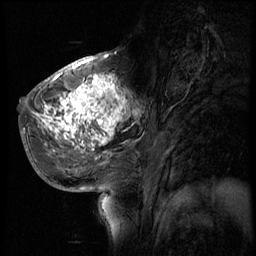
Breast MRI (dynamic contrast-enhanced), one sagittal slice. Slice 25 of 56 in the series (ordered by position). 4 images stored at this slice position (order not interpretable as contrast timing). 1.5 T. TE 4.2 ms, TR 8.9 ms. 2.5 mm slice thickness. 256 × 256 image matrix, field of view 220 × 220 mm. Patient: female, 51 years. From the clinical record (not read from this slice): setting: breast cancer imaged before/during neoadjuvant chemotherapy; receptor status: triple-negative.
Outlined on this slice (semi-automatic segmentation, software-assisted and operator-edited):
- analysis volume of interest (the breast-tissue region the enhancement analysis was run in; not a lesion): box from (x=30, y=70) to (x=150, y=173) px
- tumour enhancement mask (voxels above the 140 % enhancement threshold inside the analysis volume of interest): (x=34, y=74)–(x=127, y=147)